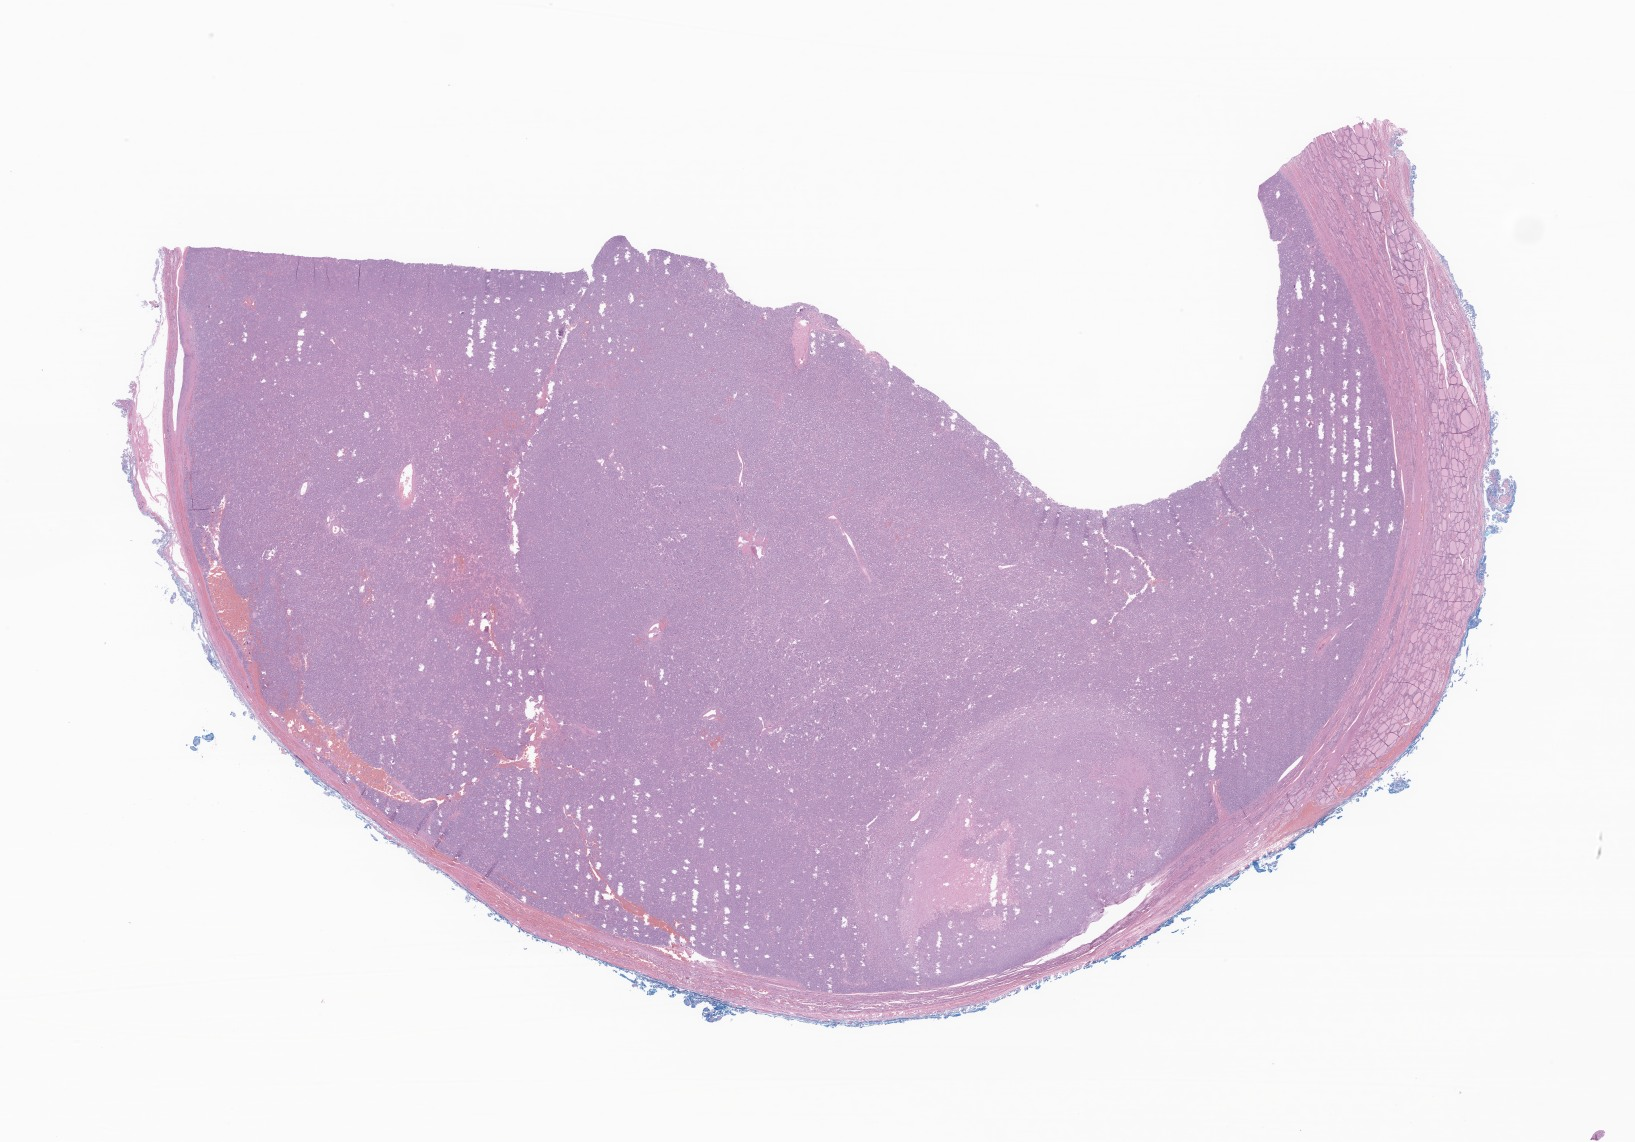
Haematoxylin and eosin whole-slide image of tumor tissue from the thyroid, a low-resolution overview of the entire scanned area, about 27.6 x 19.3 mm. Formalin-fixed, paraffin-embedded (FFPE) tissue. Patient: female, age 221 months (18 years 5 months).
• recorded diagnosis: Papillary carcinoma, follicular variant